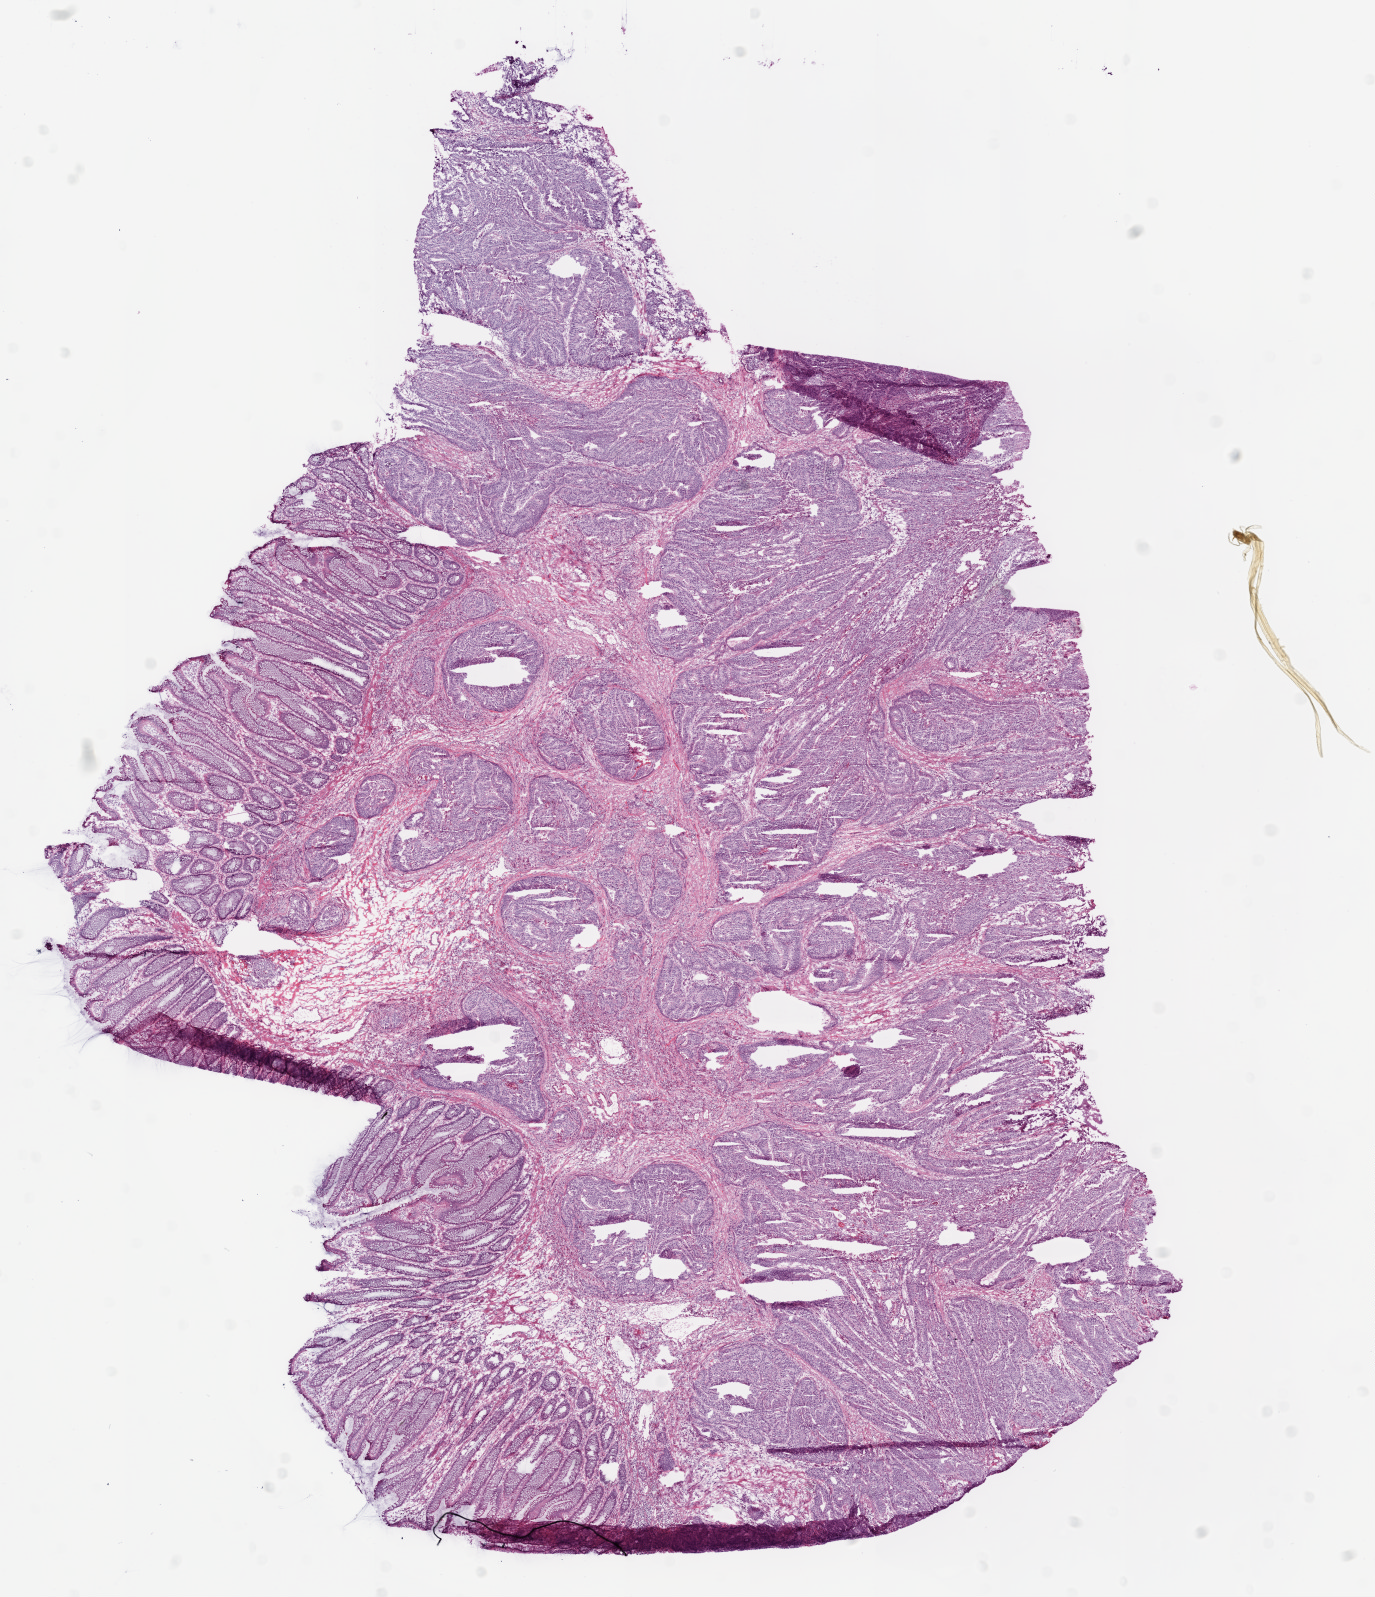
H&E whole-slide image, low-resolution overview of the scanned area, about 11.0 x 12.8 mm (from a 20x scan), frozen section, colon, primary tumour sample. Female patient; age at initial diagnosis 78 years. Pathologist review of this section (percent, as recorded): tumour cells 60%, tumour nuclei 80%, normal cells 30%, stromal cells 10%, necrosis 0%.
AJCC pathologic stage: IIIC (6th edition). Diagnosis: Adenocarcinoma, NOS.